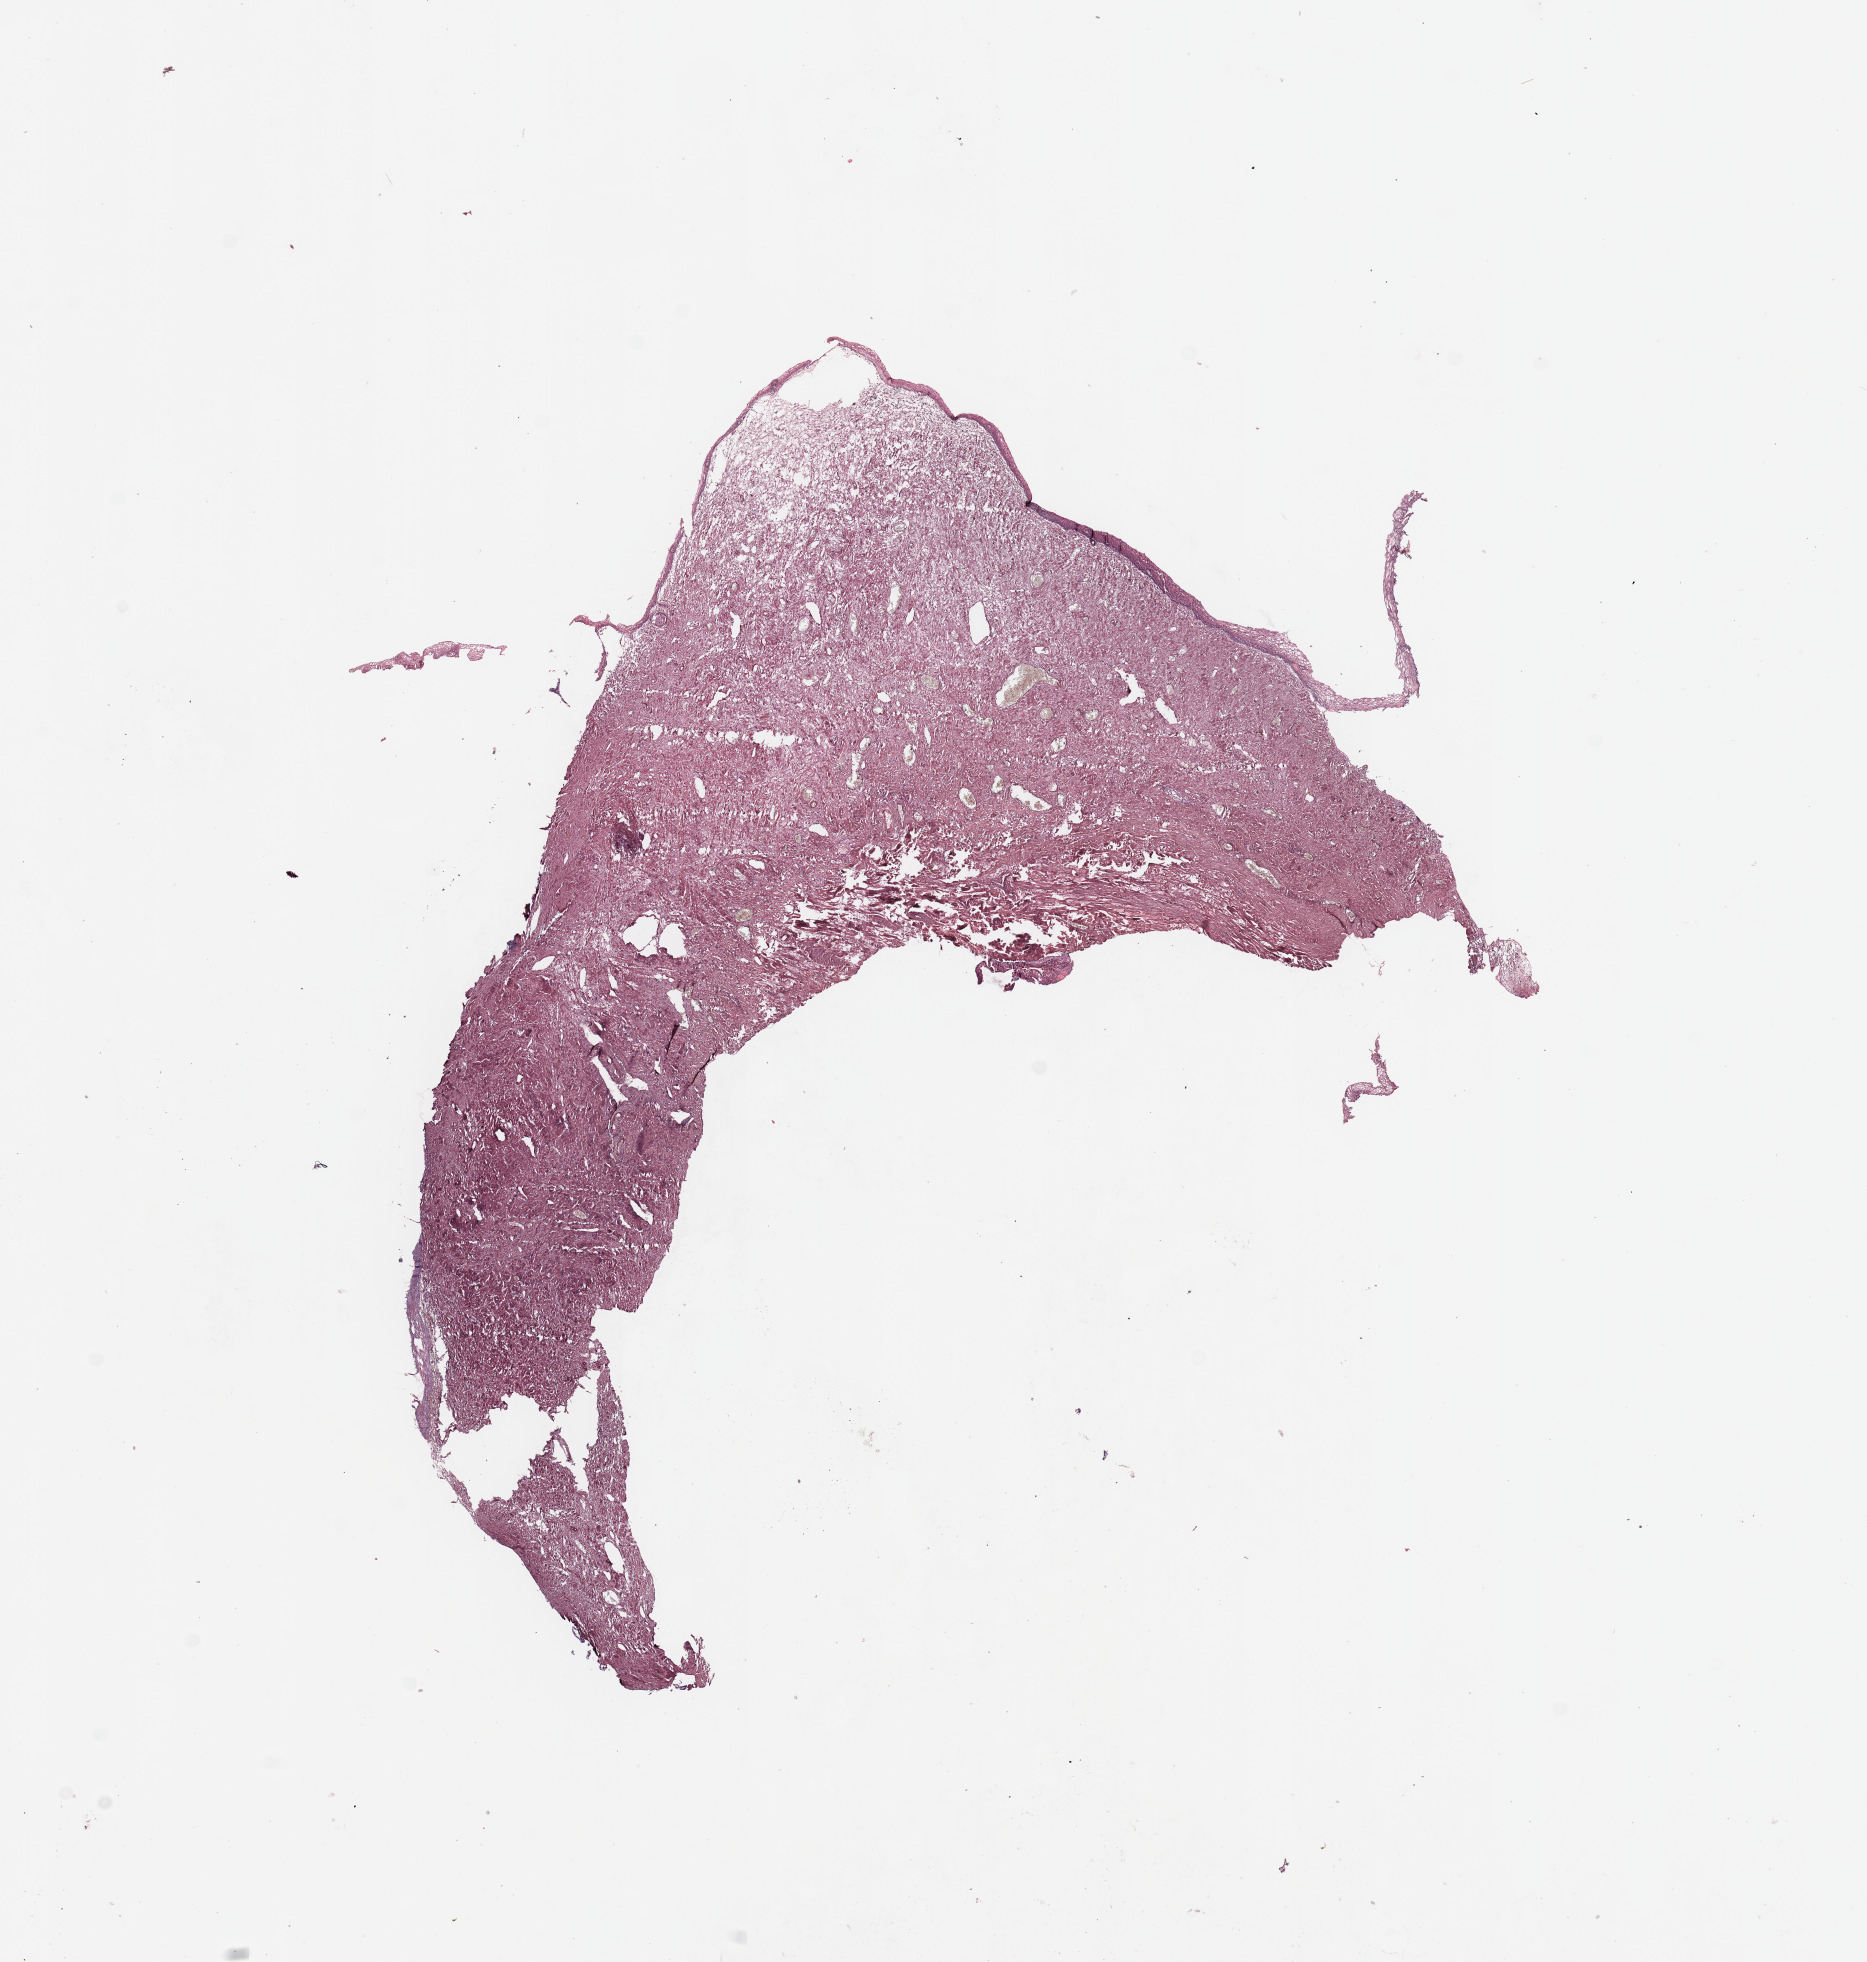
Digitized Hematoxylin and eosin (H&E) stained tissue section (whole slide), whole scanned area (about 14.8 x 15.5 mm, slide scanned at 20x) shown as a low-resolution overview. Uterus, normal (non-tumour) tissue. Female, 67 y/o.
* this section: normal (non-tumour) tissue from the same patient
* patient diagnosis: Endometrioid adenocarcinoma, NOS